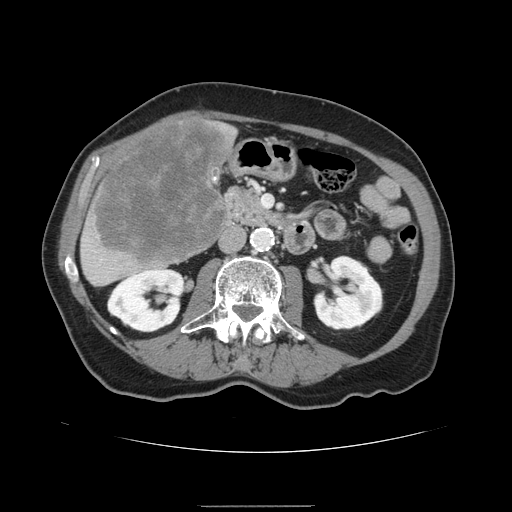
Contrast-enhanced abdominal CT, one axial slice. Slice 52 of 168 in the series (ordered by position). Intravenous contrast given. Soft-tissue window (W 400 / L 40 HU). 2.5 mm slice thickness. 512 × 512 image matrix, field of view 386 × 386 mm. Male patient, age 74 years. From the clinical record (not read from this slice): diagnosis: colorectal cancer liver metastases, imaged before liver resection; multiple liver metastases: no; largest metastasis: 14.5 cm.
Structures marked on this image (expert manual segmentation):
- liver: bounding box (x1, y1, x2, y2) in pixels: (80, 116, 238, 287)
- liver metastasis: (93, 122, 231, 265)